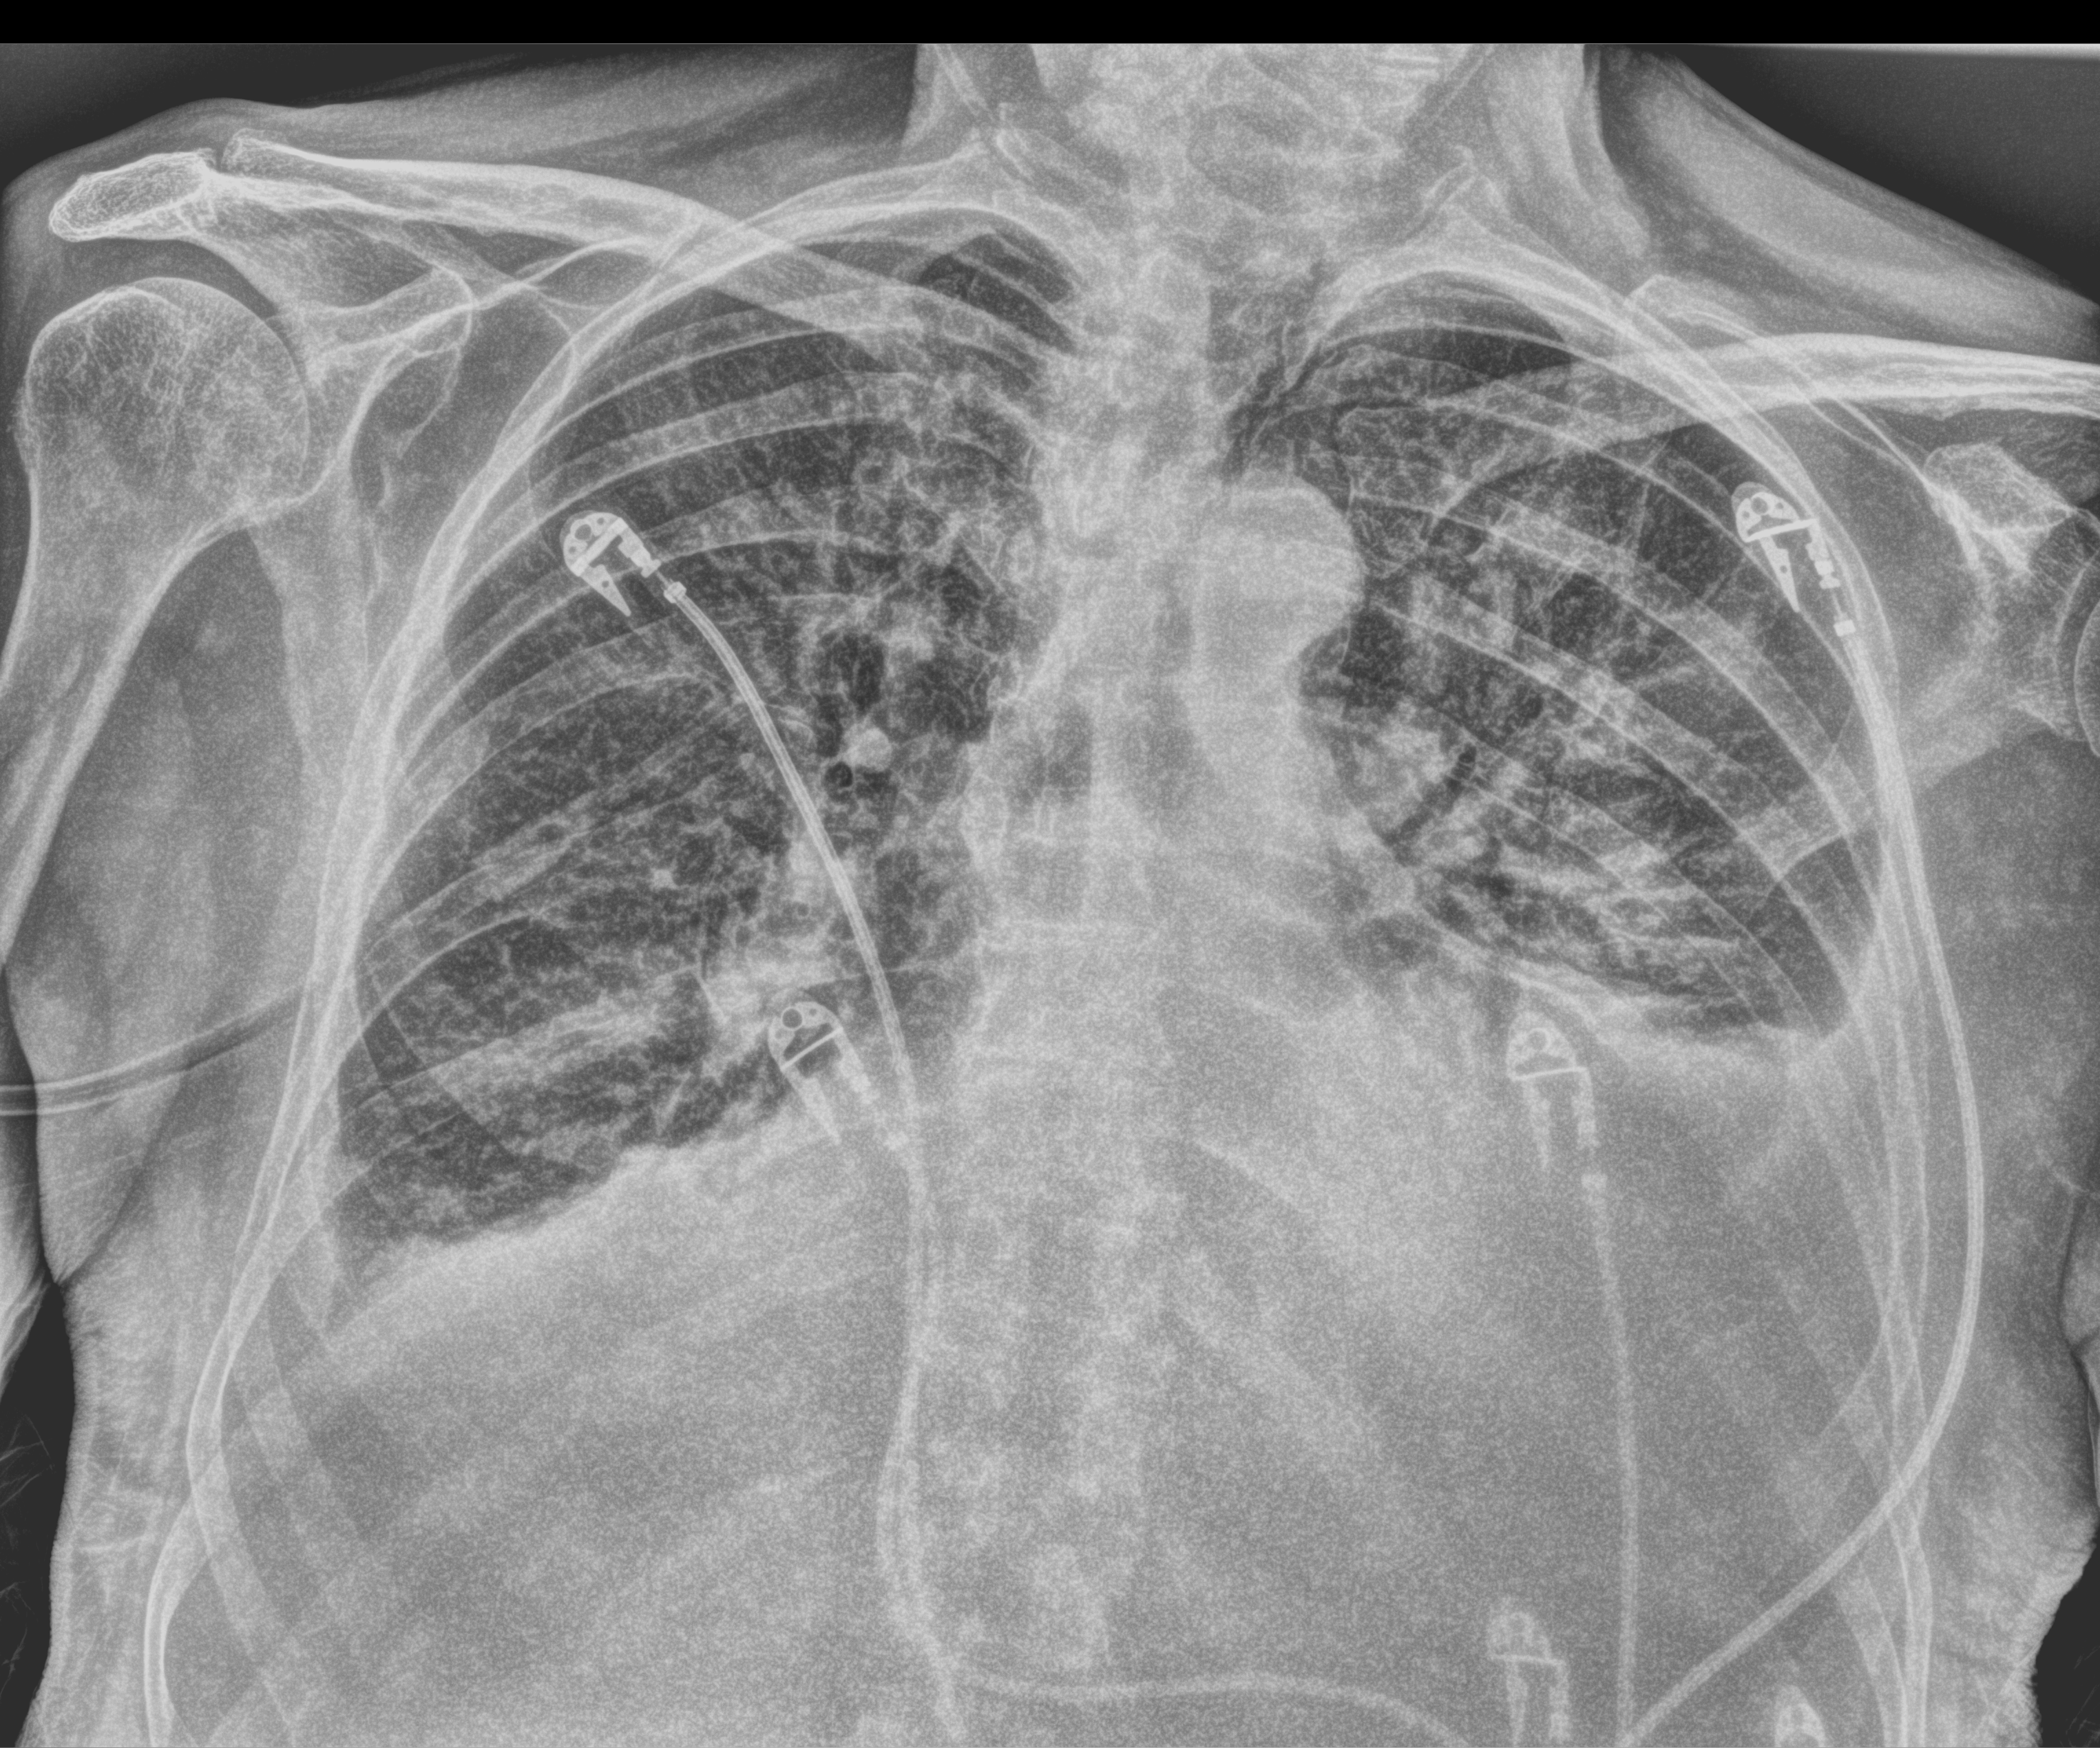
Chest X-ray (portable), anteroposterior (AP) projection. Male patient hospitalised with COVID-19, age 75–90 years.
Hospital-stay facts (about this admission, not read from this image; timing relative to this image not recorded): length of hospital stay: 3 days; admitted to intensive care during this hospital stay: no.